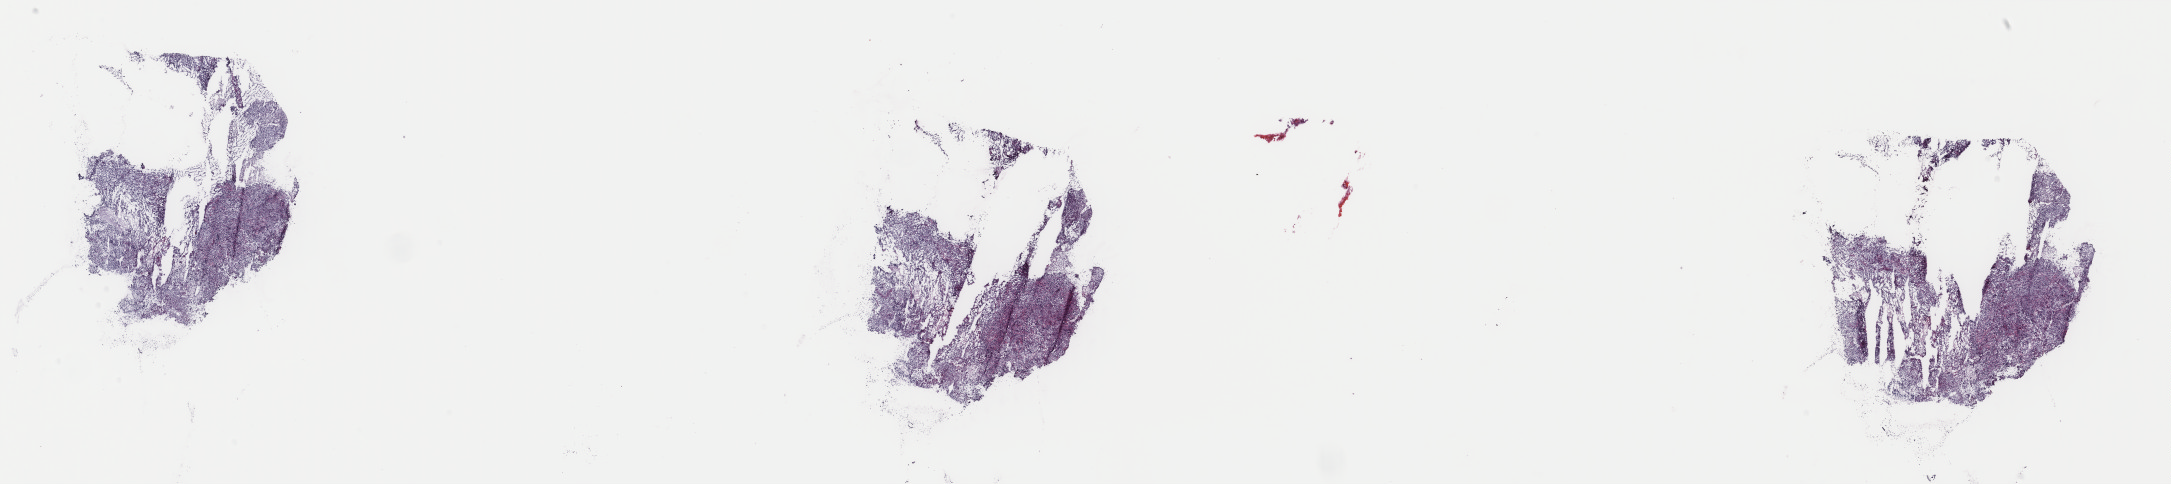
Hematoxylin and eosin (H&E) stained whole-slide image, low-resolution overview of the scanned area, about 34.5 x 7.7 mm (acquisition: 40x scan). Frozen section from the top of the tissue portion. Primary tumour sample from the lymphoid tissue. Female patient; age at initial diagnosis 62 years. Slide review estimates, as recorded: tumour cells 65%, tumour nuclei 70%, normal cells 15%, stromal cells 15%, necrosis 5%. Infiltration values recorded for this section: lymphocyte infiltration 80%, monocyte infiltration 10%, neutrophil infiltration 0%.
• diagnosis: Primary diffuse large B-cell lymphoma of the CNS (bones of skull and face and associated joints)